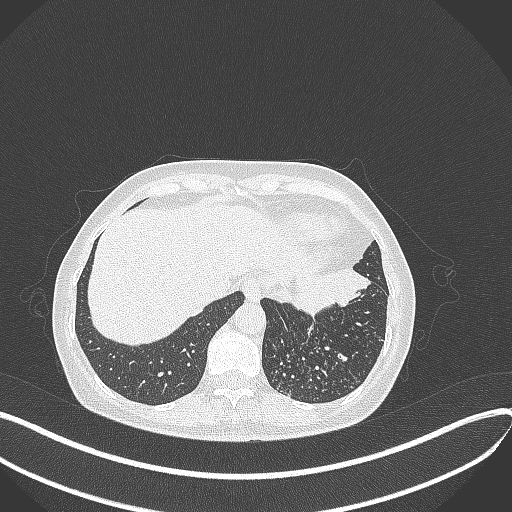
Chest CT, one axial slice; position 85 of 429 along the scan axis; reconstruction kernel B70f; lung window (W 1500 / L -600 HU); 1 mm slice thickness; 512 × 512 image matrix, field of view 400 × 400 mm. Patient: female, 63 years. Case-level facts recorded for this patient, not image findings: clinical TNM (as recorded): T1b N0 M0.
Structures marked on this image (rectangle marked by the reading radiologist):
- lung tumour (recorded histology: adenocarcinoma): box from (x=291, y=268) to (x=375, y=315) px